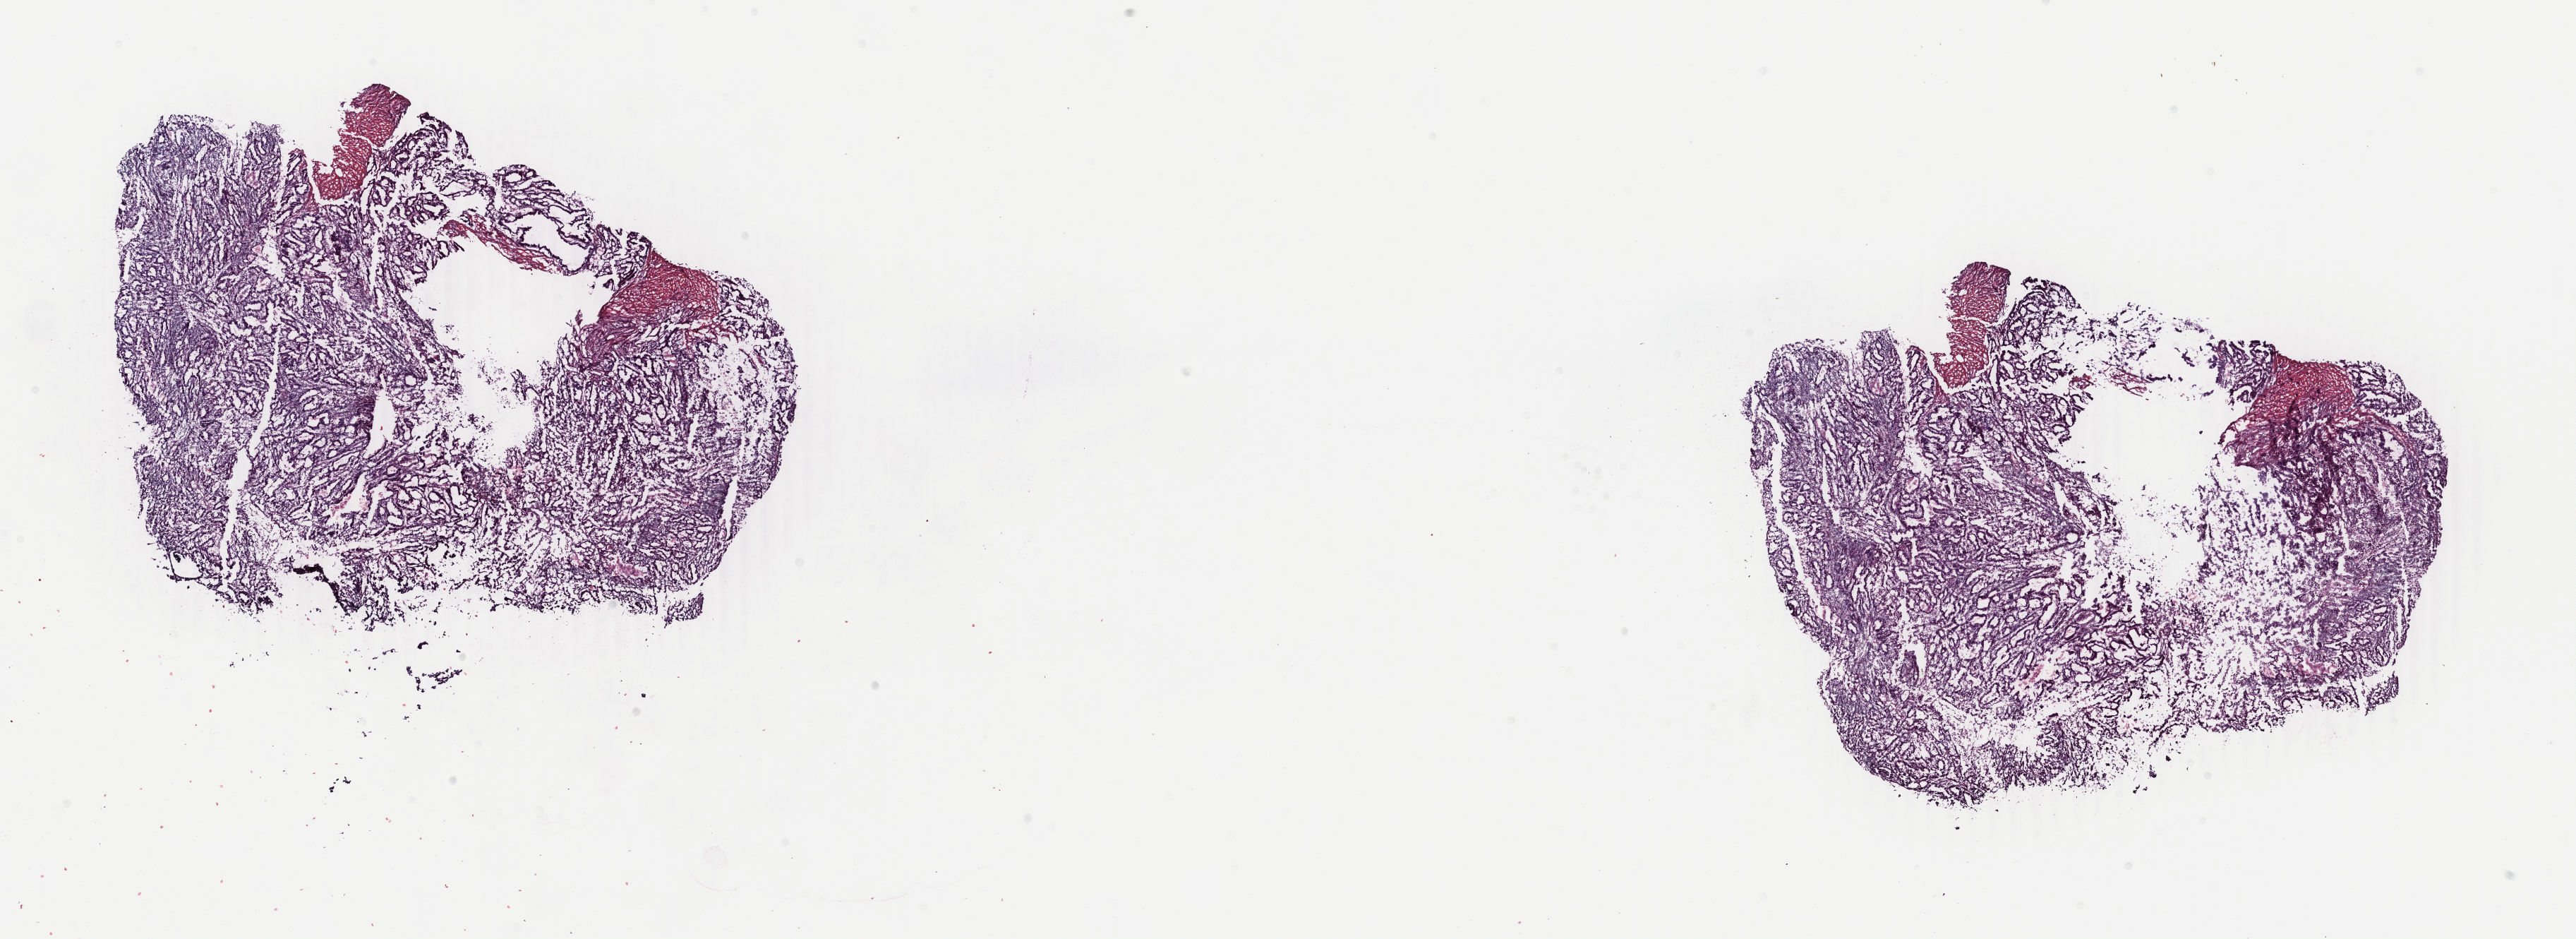
H&E whole-slide image, shown as a low-resolution overview of the whole scanned area (about 29.0 x 10.6 mm, acquisition: 40x scan), frozen section, sample: primary tumour, uterus. Female, age 68 years at initial diagnosis. Histologic grade: G2 (moderately differentiated). Composition of this section per pathologist review: tumour cells 85%, tumour nuclei 80%, normal cells 0%, stromal cells 5%, necrosis 10%. Inflammatory infiltration, as recorded: lymphocyte infiltration 20%, monocyte infiltration 20%, neutrophil infiltration 40%.
- diagnosis: Endometrioid adenocarcinoma, NOS (endometrium)
- FIGO stage: IB